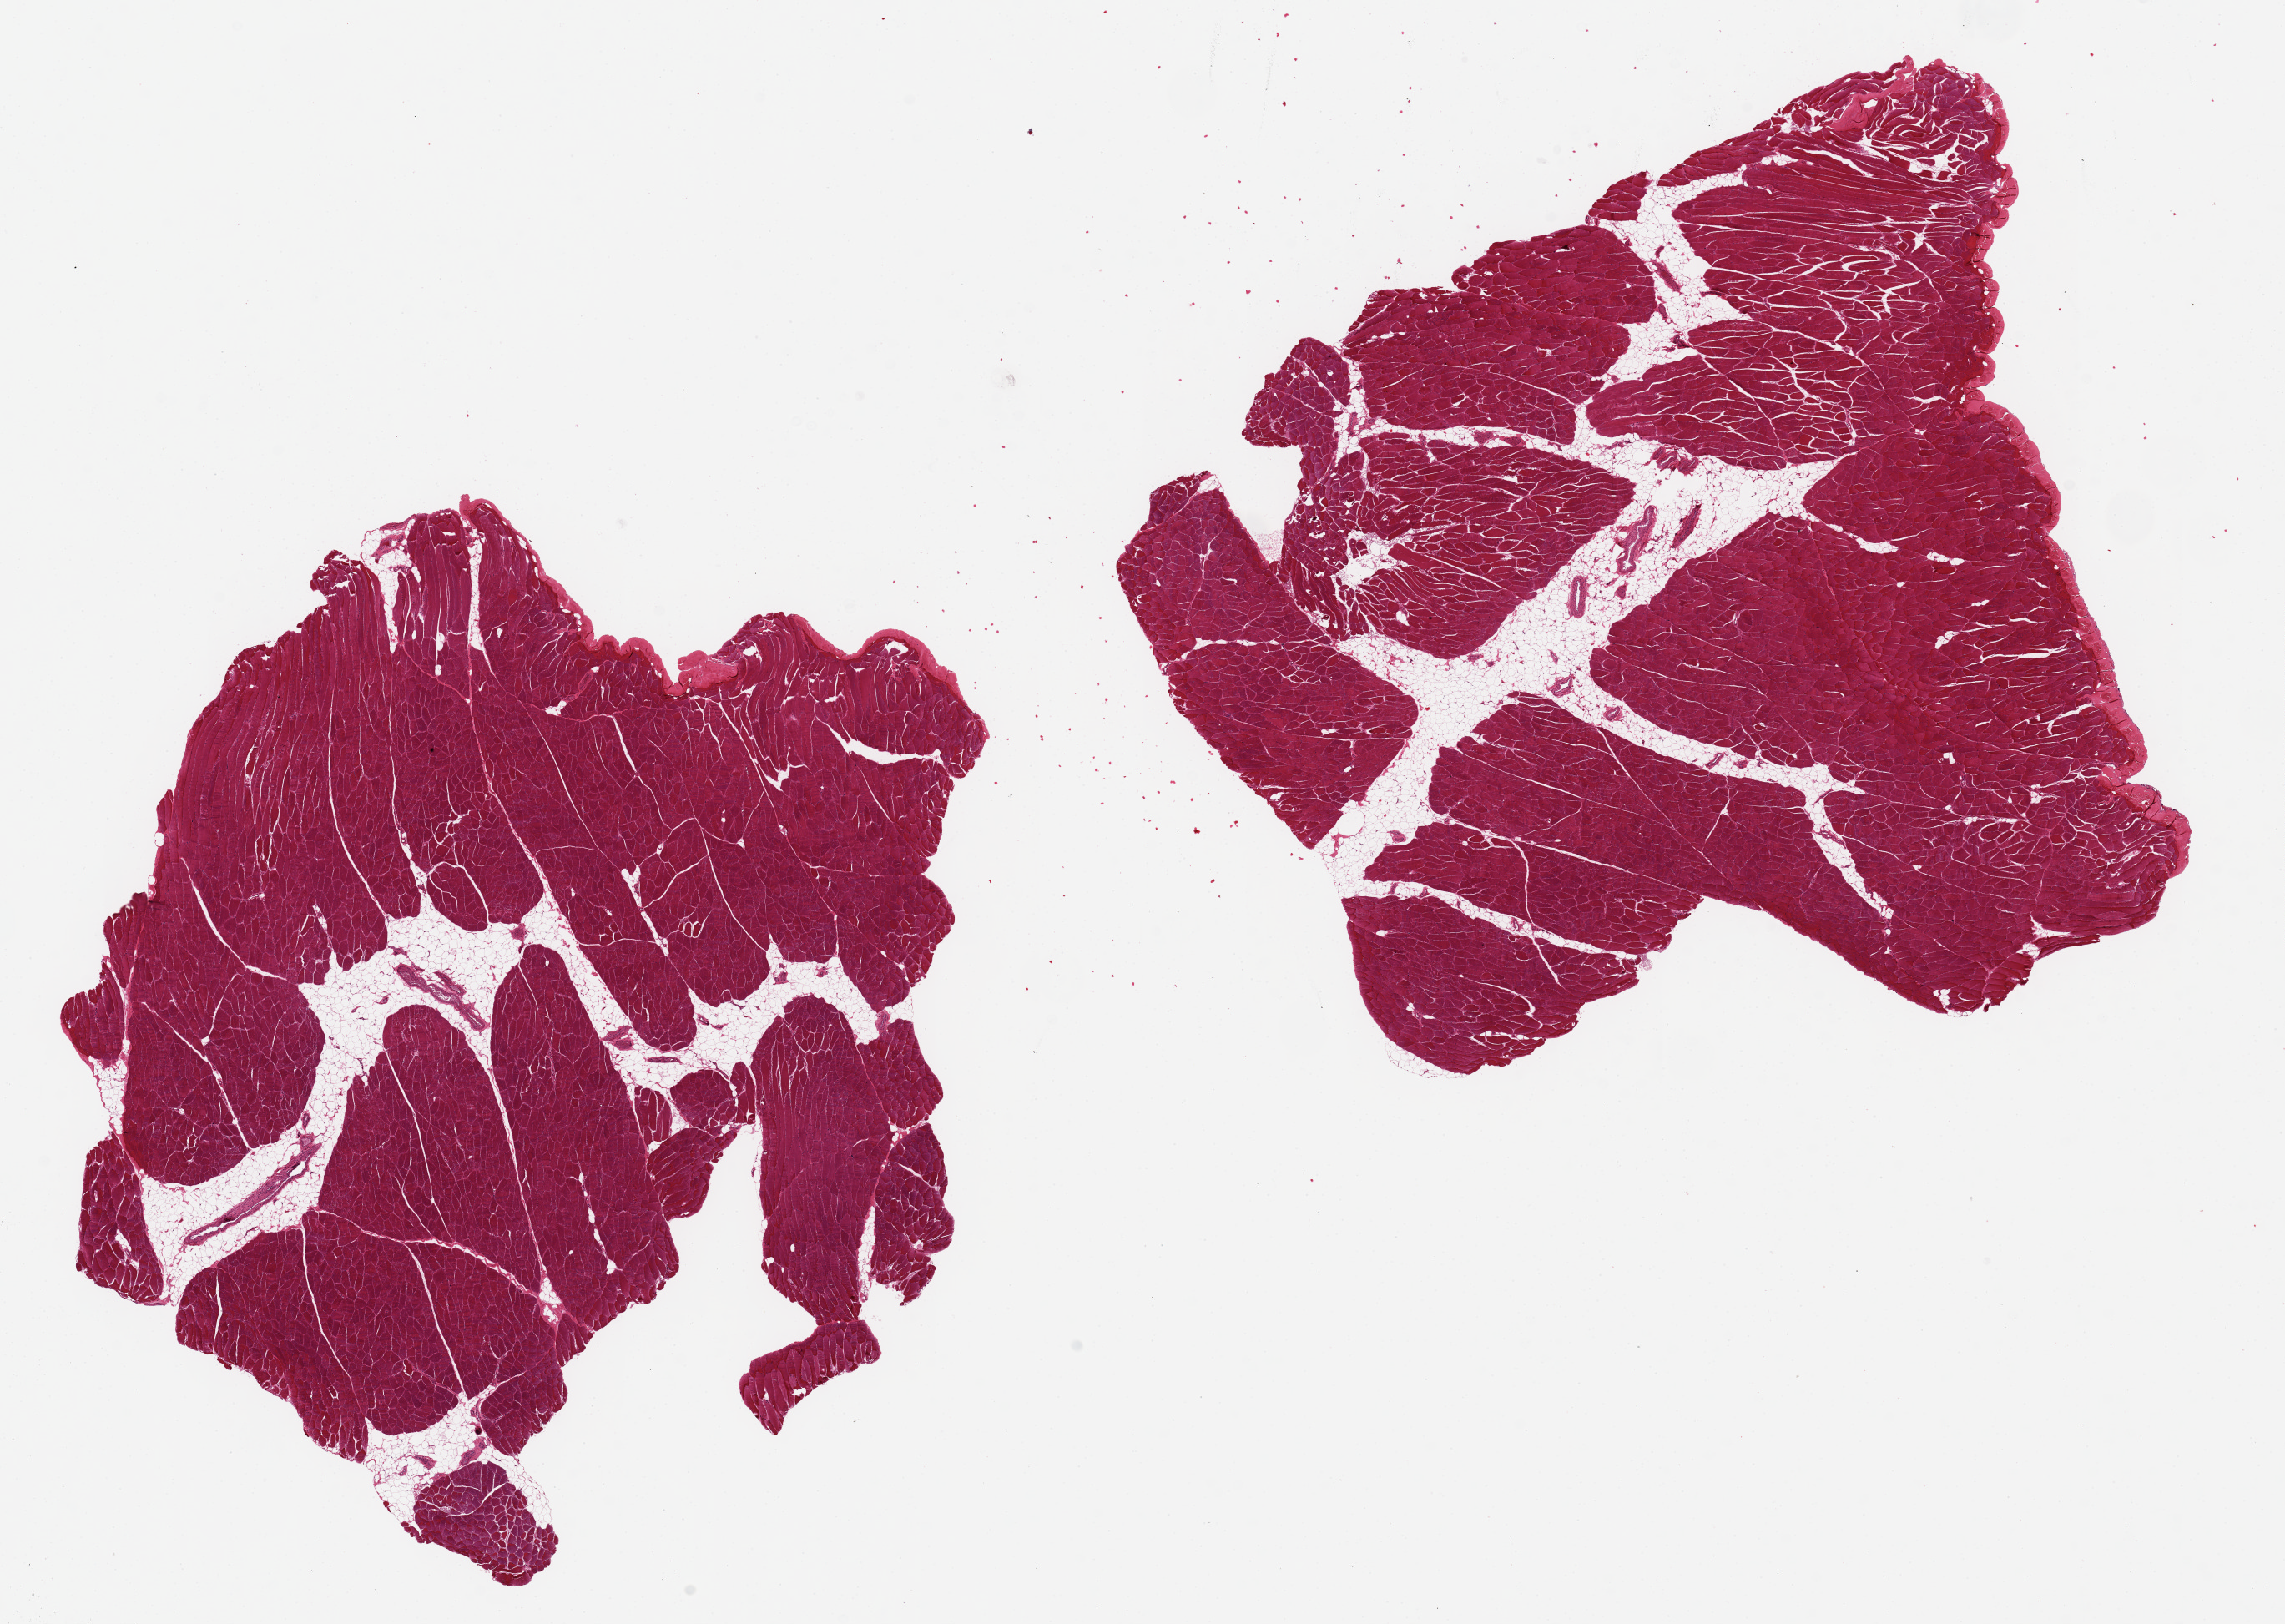
Hematoxylin and eosin (H&E) whole-slide image, whole scanned area (about 21.7 x 15.4 mm) shown as a low-resolution overview. PAXgene-fixed paraffin-embedded (PFPE) section. Sampled site (target tissue): skeletal muscle. Donor tissue sample. Donor sex: male.
• review note (as recorded): 2 ~9x7.5mm aliquots. Interstitial fat ~10% of specimens